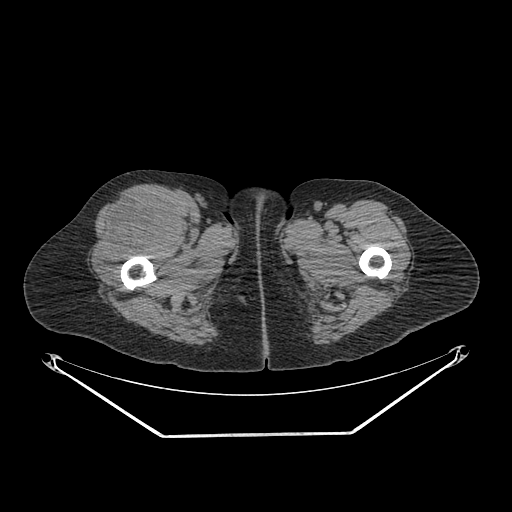
CT of an extremity soft-tissue mass (from a PET/CT study), one axial slice; position 273 of 311 along the scan axis; reconstruction kernel SOFT; soft-tissue window (W 400 / L 40 HU); 3.75 mm slice thickness; 512 × 512 image matrix, field of view 500 × 500 mm. Female patient. Case-level facts recorded for this patient, not image findings: histological type: pleiomorphic undifferentiated sarcoma; grade: high; site of the primary tumour: right quadricep.
Outlined on this slice (expert contour drawn on MRI and transferred to this co-registered scan by the dataset authors):
- tumour plus oedema (research contour): bounding box <96,194,175,273> (left, top, right, bottom; pixels)
- tumour (research contour): <96,194,175,273>